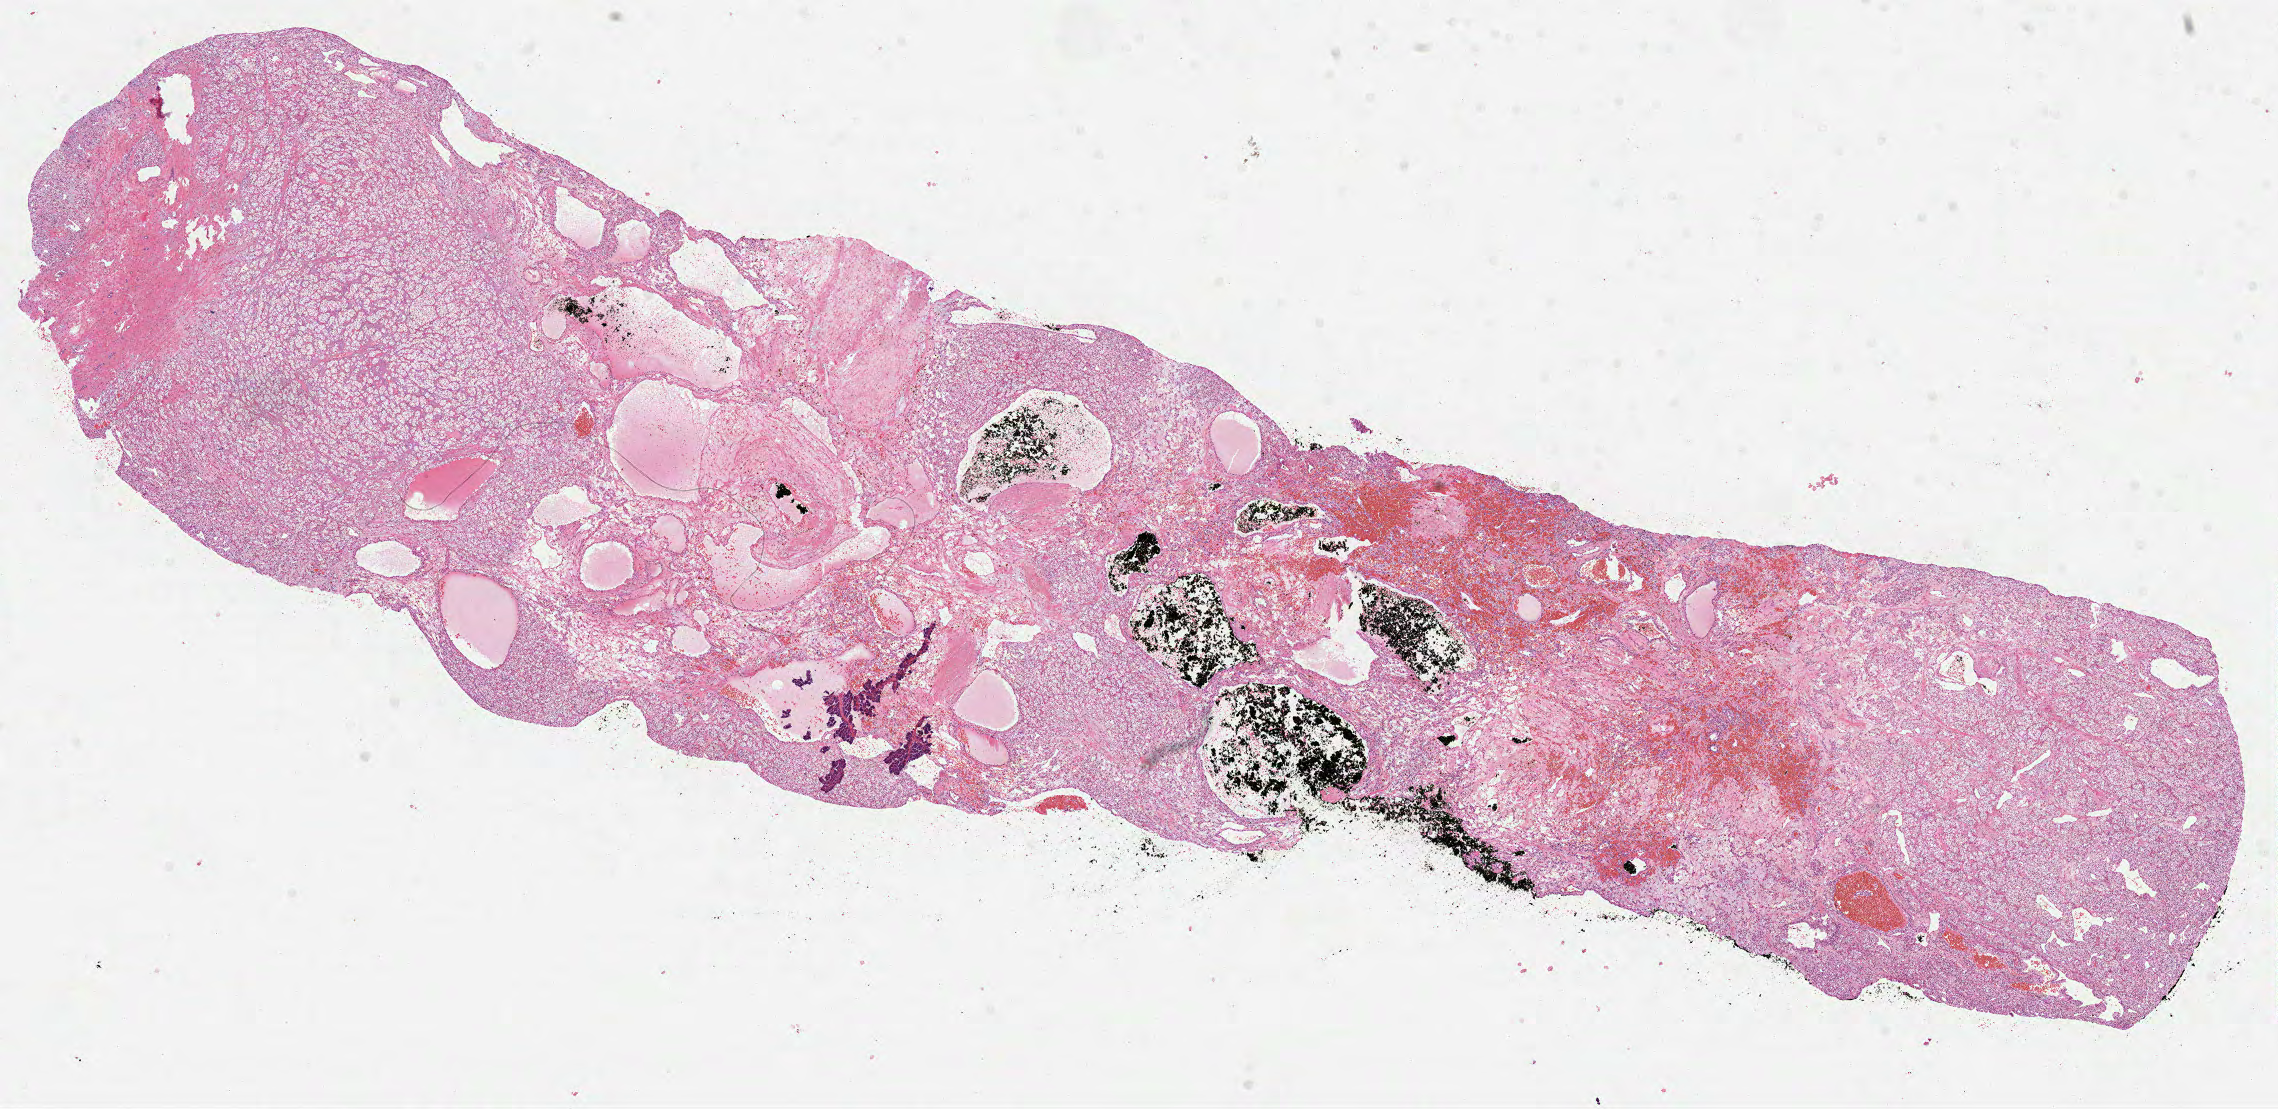
H&E whole-slide image — a low-resolution overview of the entire scanned area, about 18.4 x 8.9 mm (from a 40x scan). Formalin-fixed paraffin-embedded (FFPE) diagnostic section. Kidney, primary tumour sample. Male, age 51 years at initial diagnosis. Histologic grade: G2 (moderately differentiated).
* AJCC pathologic stage: I
* histologic diagnosis: Clear cell adenocarcinoma, NOS
* laterality: left